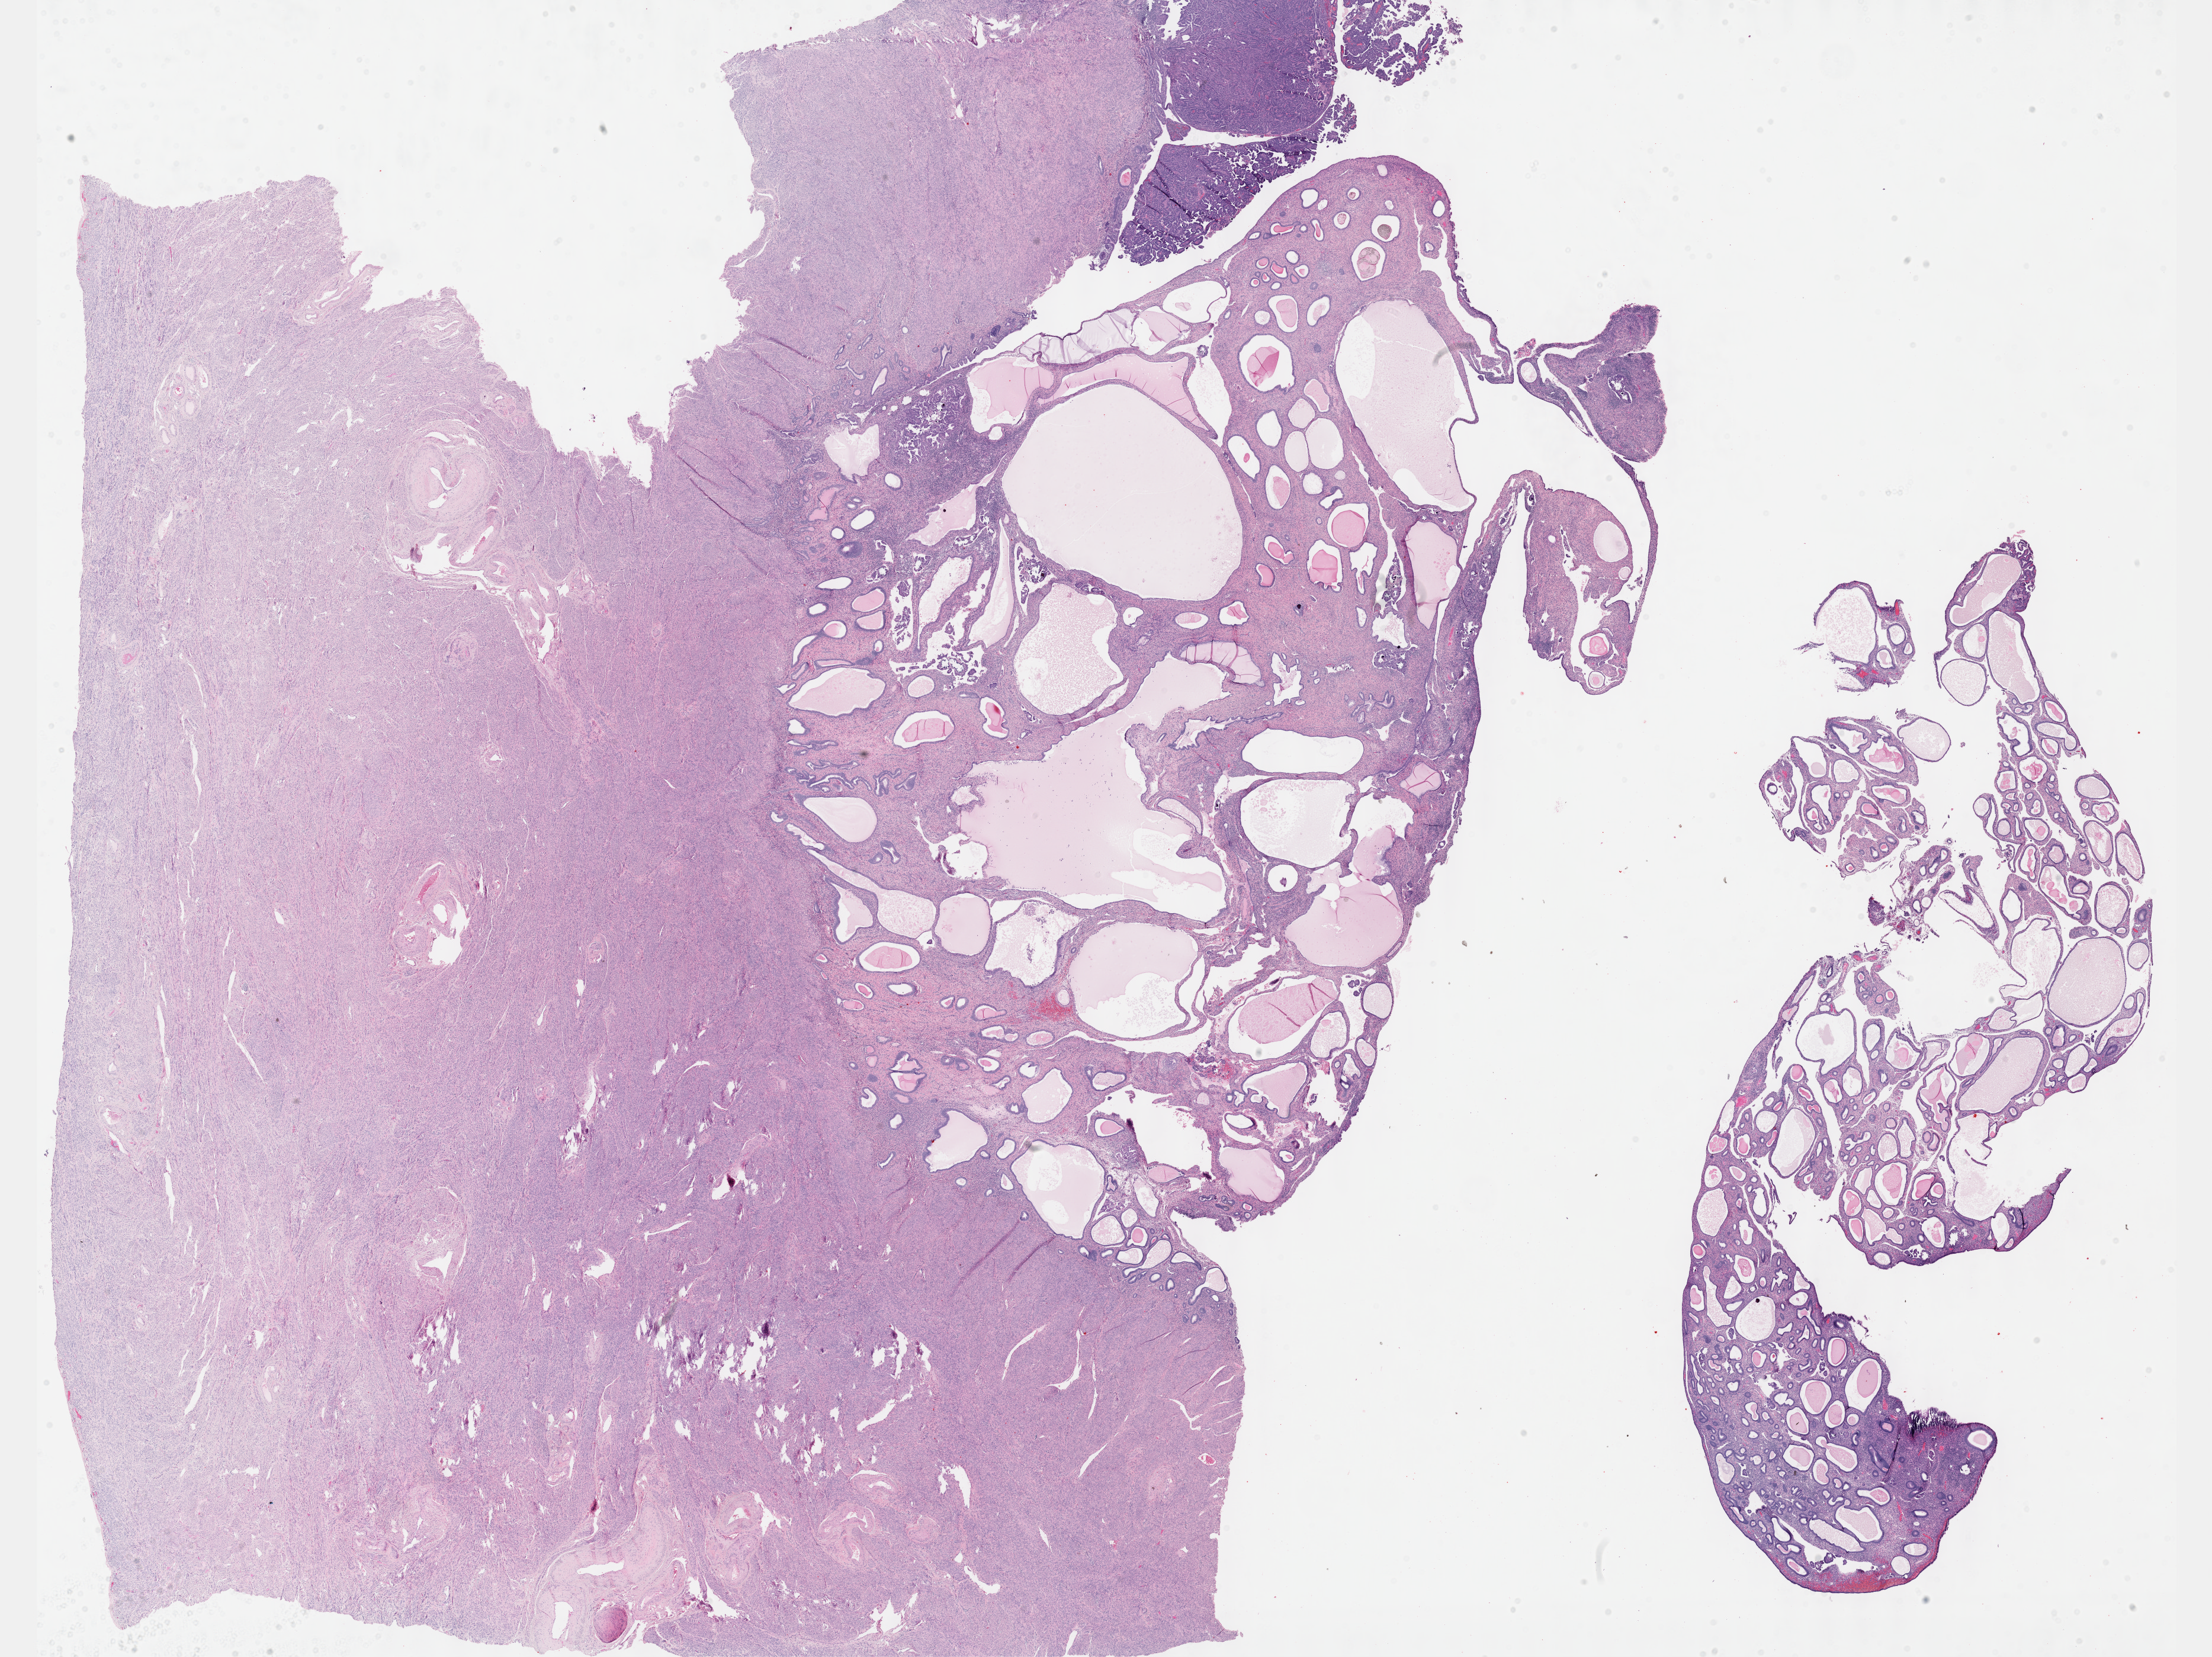
Whole-slide histology image, H&E, a low-resolution overview of the entire scanned area, about 30.2 x 22.6 mm. Formalin-fixed paraffin-embedded (FFPE) diagnostic section. Primary tumour sample from the uterus. Female, age 73 years at initial diagnosis. Histologic grade: G3 (poorly differentiated).
* FIGO stage: IA
* diagnosis: Serous surface papillary carcinoma (endometrium)